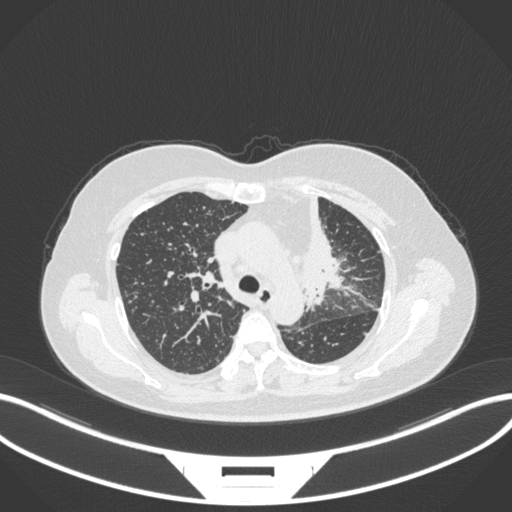
Chest CT, one axial slice; 120 kVp; lung window (W 1500 / L -600 HU); 1 mm slice thickness; 512 × 512 image matrix, field of view 400 × 400 mm. Female patient, age 49 years. Case-level facts recorded for this patient, not image findings: clinical TNM (as recorded): T1c N0 M1.
Structures marked on this image (bounding box drawn by a radiologist):
- lung tumour (recorded histology: adenocarcinoma): bounding box [x1, y1, x2, y2] px = [285, 189, 346, 314]